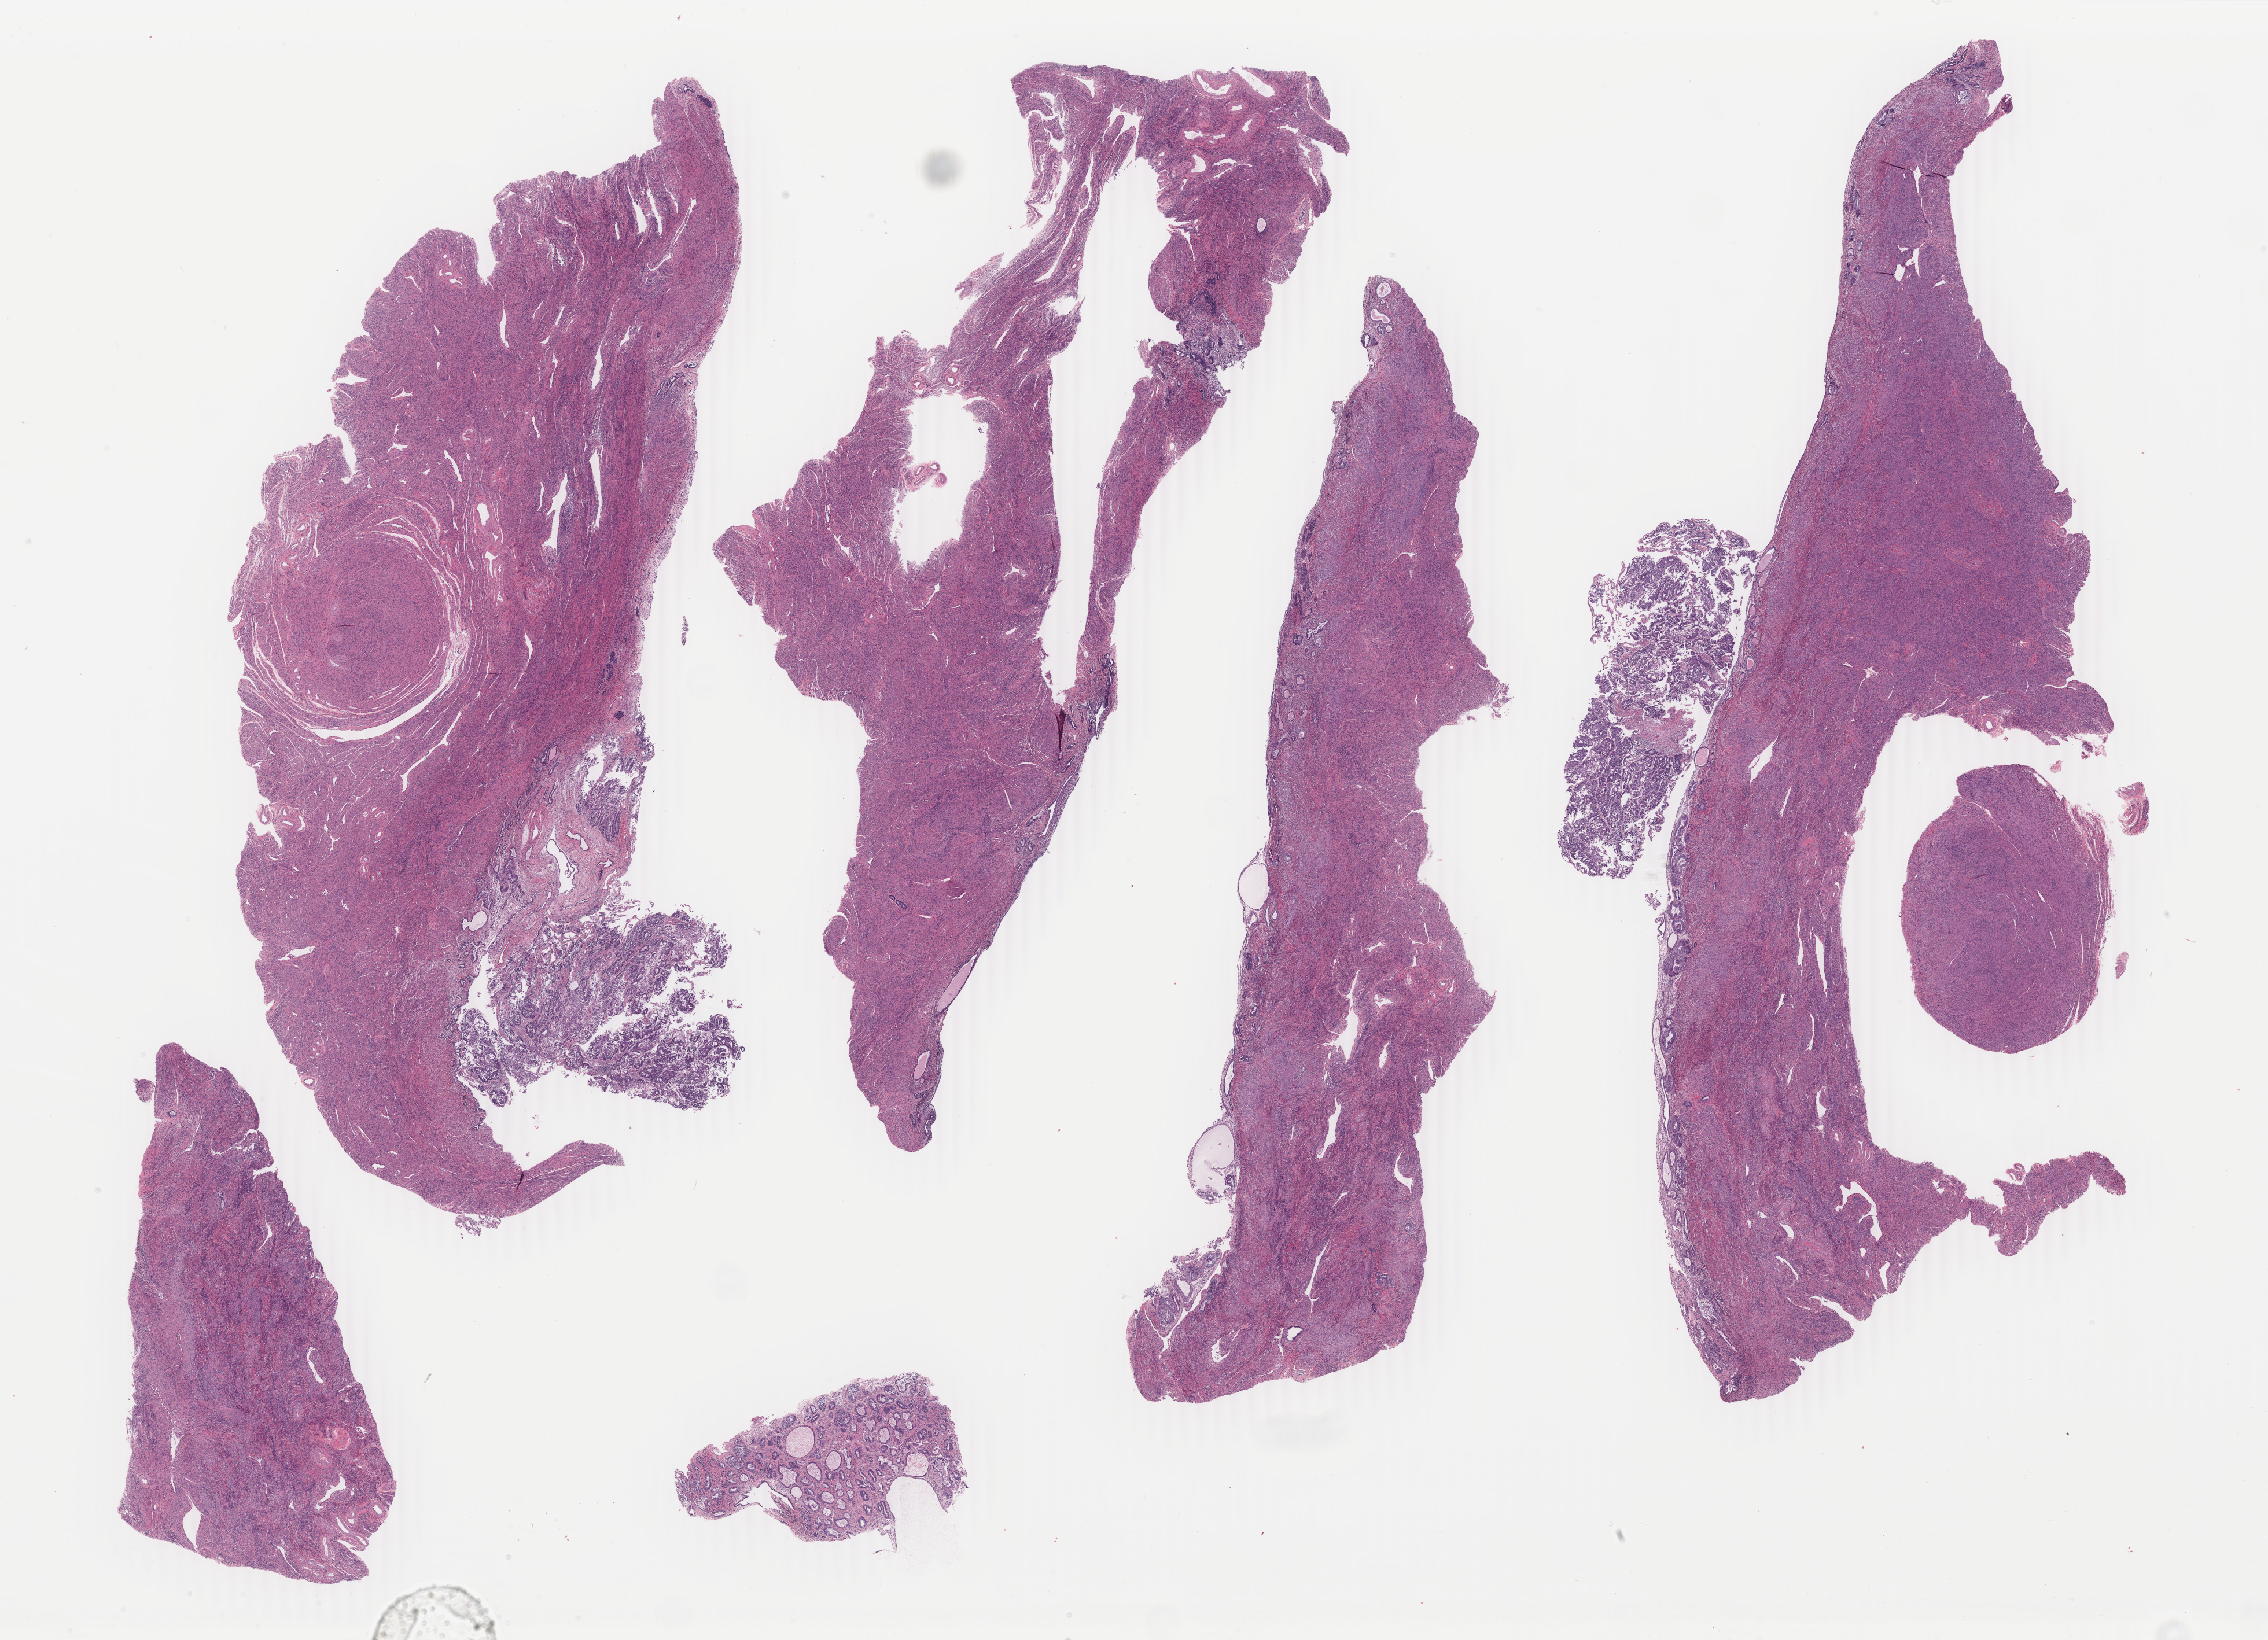
H&E-stained whole-slide image — a low-resolution overview of the entire scanned area, about 31.2 x 22.5 mm (slide scanned at 40x), formalin-fixed paraffin-embedded (FFPE) diagnostic section, uterus, primary tumour sample. Female, age 74 years at initial diagnosis.
Pathologic diagnosis: Endometrioid adenocarcinoma, NOS (endometrium).